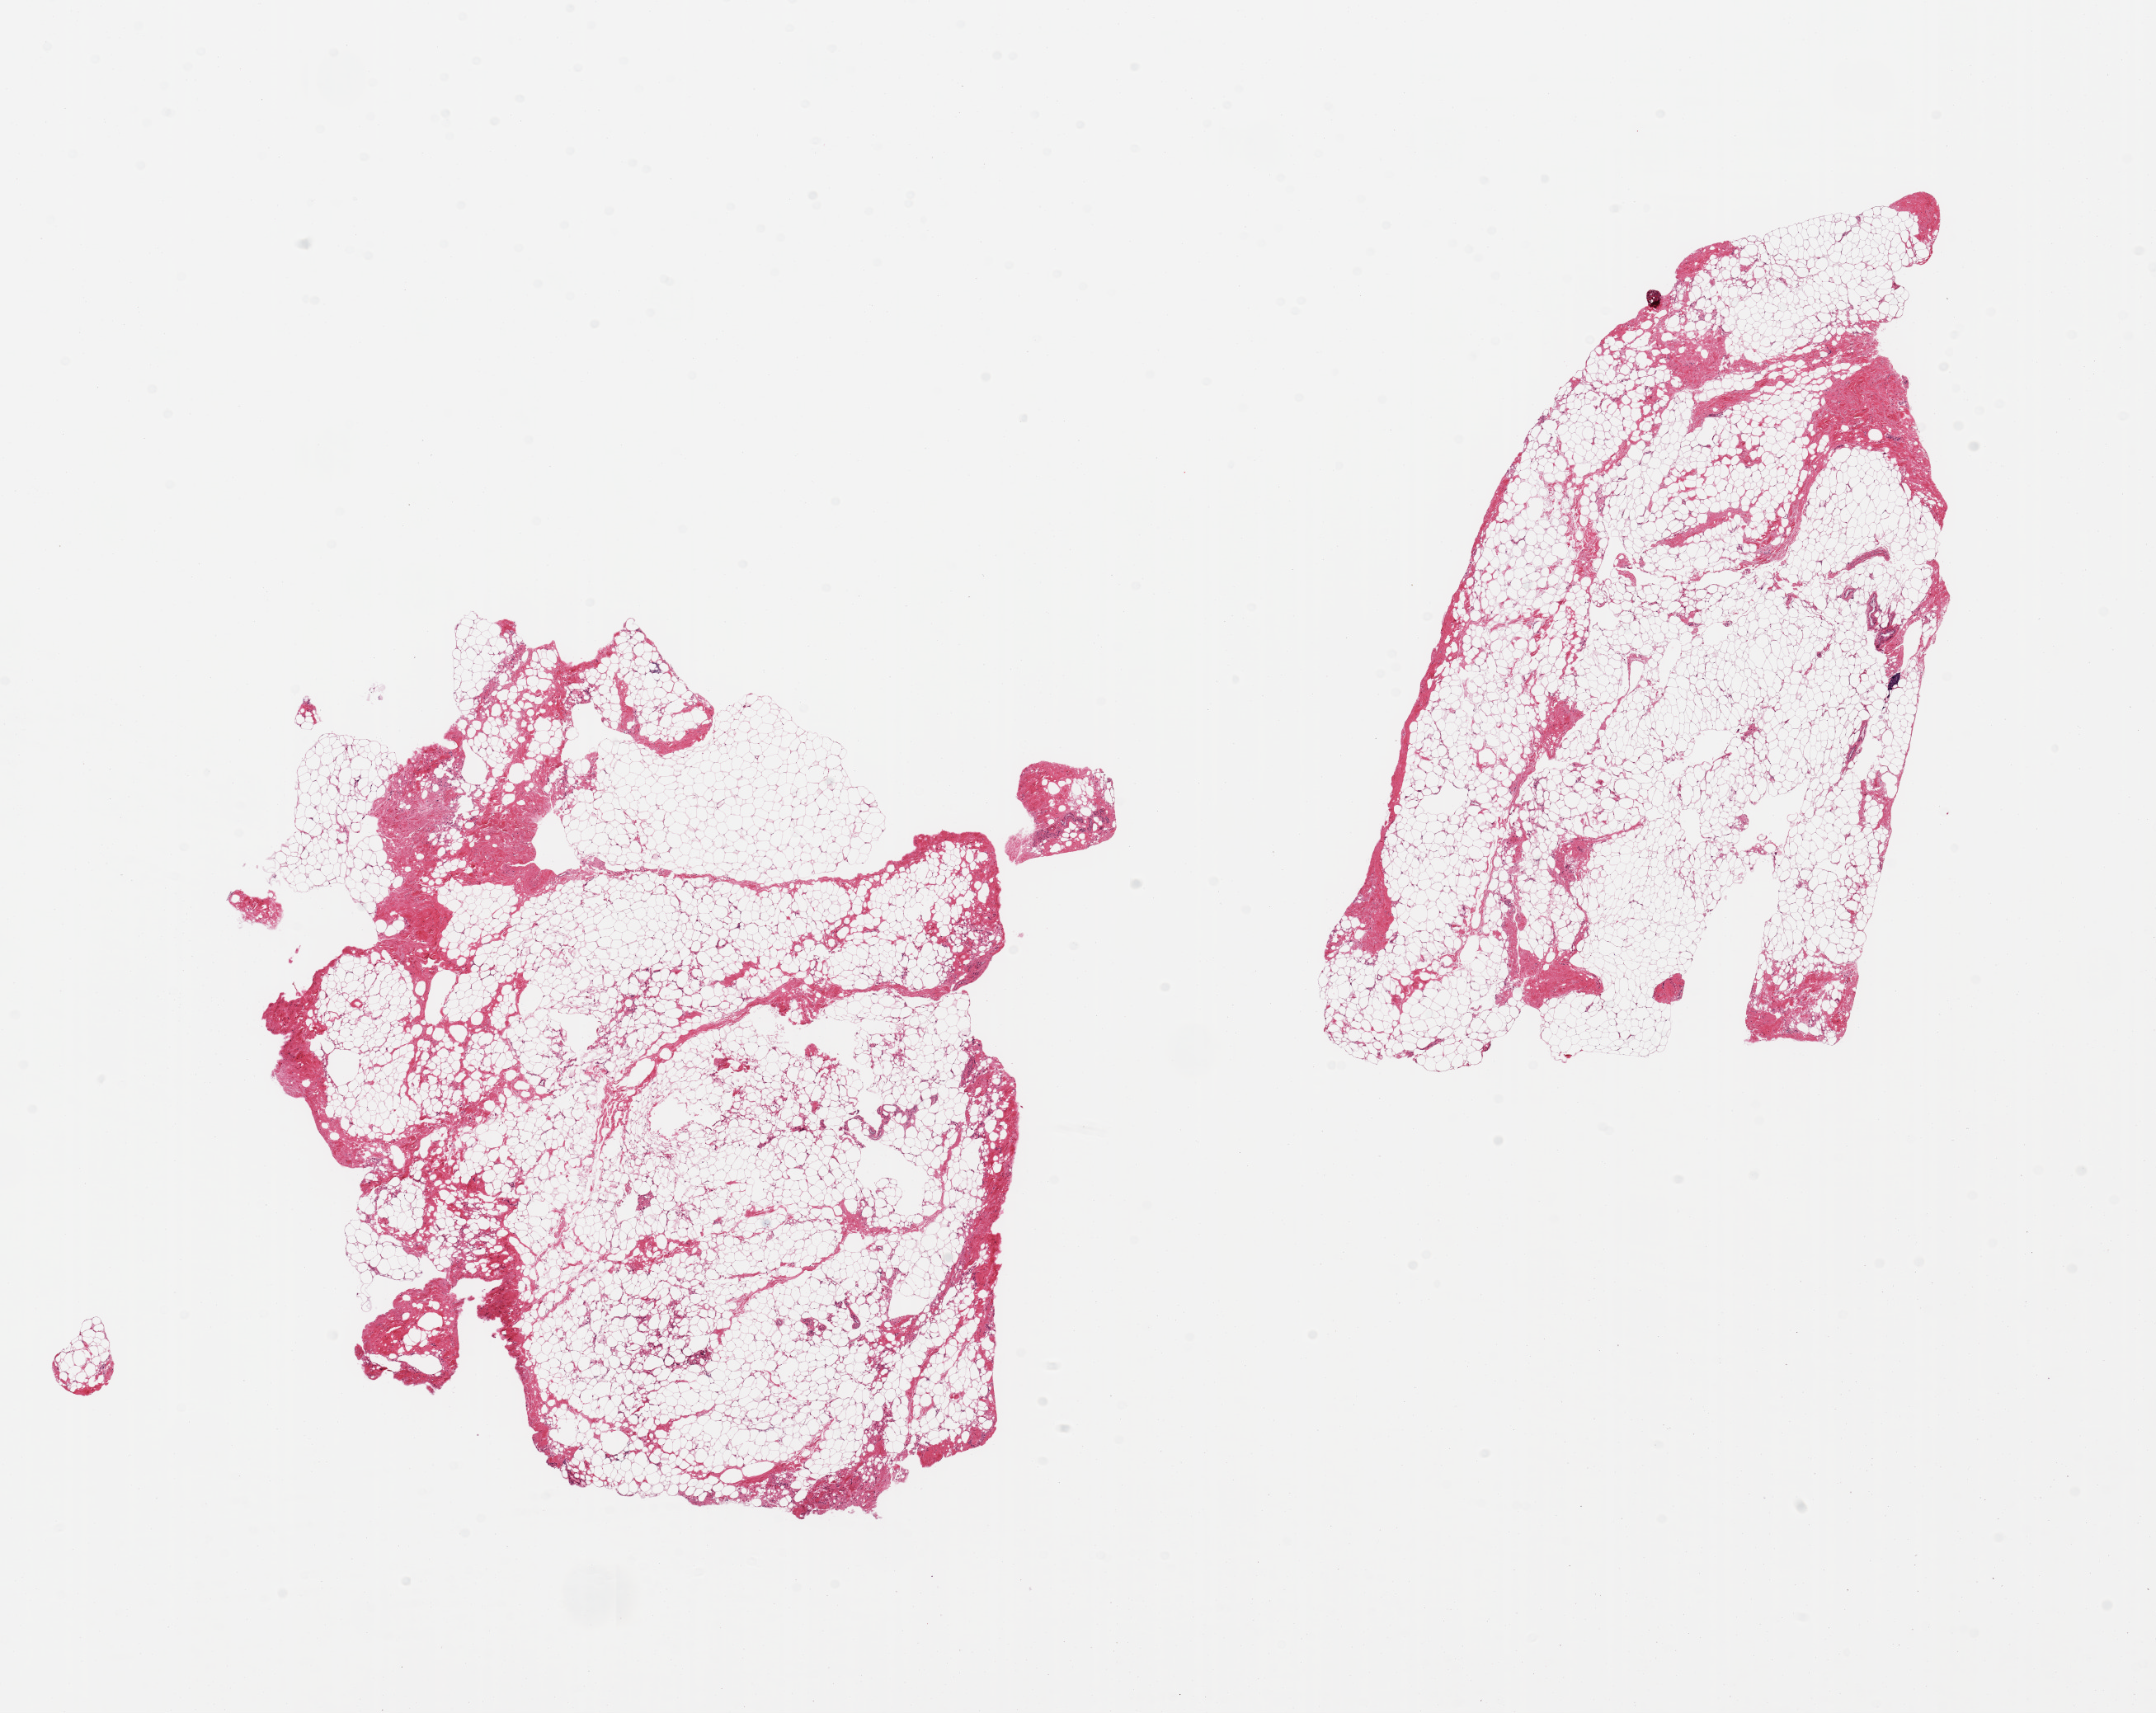
Digitized haematoxylin and eosin-stained section, brightfield, low-resolution overview of the scanned area, about 20.7 x 16.4 mm, PAXgene-fixed, paraffin-embedded tissue, sampled site (target tissue): breast, tissue donor sample. Male donor.
Review note (as recorded): 2 pieces; fibrofatty tissue with no mammary ducts.